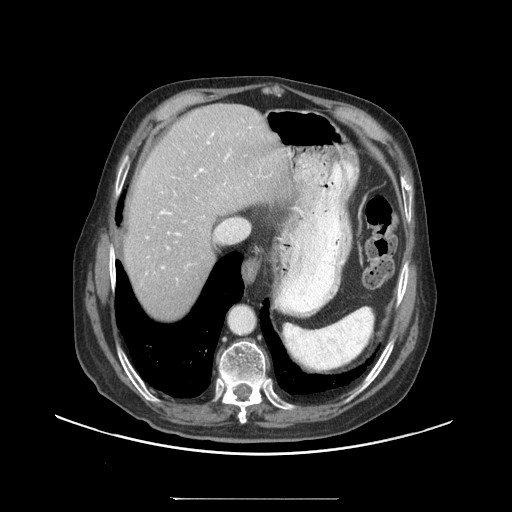
Contrast-enhanced abdominal CT (liver protocol), one axial slice. Position 80 of 97 along the scan axis. Reconstruction kernel STANDARD. Soft-tissue window (W 400 / L 40 HU). 512 × 512 image matrix, field of view 450 × 450 mm. From the clinical record (not read from this slice): diagnosis: hepatocellular carcinoma (patient treated with transarterial chemoembolisation; whether this scan precedes or follows treatment is not stated here); TNM stage (as recorded): Stage-IIIC; Child-Pugh class: A; tumour differentiation: well differentiated; tumour size: 9.2 cm.
Outlined on this slice (semi-automatic segmentation, software-assisted and operator-edited):
- abdominal aorta: bounding box (x1, y1, x2, y2) in pixels: (230, 305, 256, 333)
- liver parenchyma outside the tumour (the mass and vessels are separate outlines, so this box may not span the whole liver): (124, 104, 292, 318)
- liver vessels: (146, 126, 252, 269)